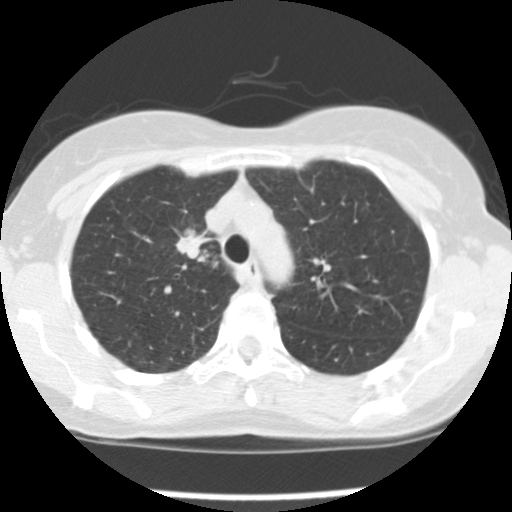
Chest CT (low-dose screening protocol), one axial image; first (baseline) screen; lung window (W 1500 / L -600 HU); standard (soft-tissue) reconstruction kernel (STANDARD); 512 × 512 image matrix, field of view 282 × 282 mm. Female participant, aged 57 years at enrolment. Current smoker at enrolment.
Lesion marked by an expert reader, bounding box [x1, y1, x2, y2] px = [166, 227, 217, 272]. The exam's reader record, not a measurement of the box and not confirmed to be the same lesion: non-calcified nodule or mass ≥4 mm, left upper lobe, 7 × 6 mm, poorly defined margins, ground glass attenuation. Note: the box lies in the patient's right hemithorax on this image, whereas the reader's record names the left lung; they may be different findings. Official screen result: positive, change unspecified: nodule(s) >= 4 mm or enlarging nodule(s), mass(es), or other non-specific abnormalities suspicious for lung cancer. Lung cancer was diagnosed 15 days after this screen: adenocarcinoma, NOS, right upper lobe, moderately differentiated (G2), stage IA (AJCC 6th edition), 15 mm at pathology.